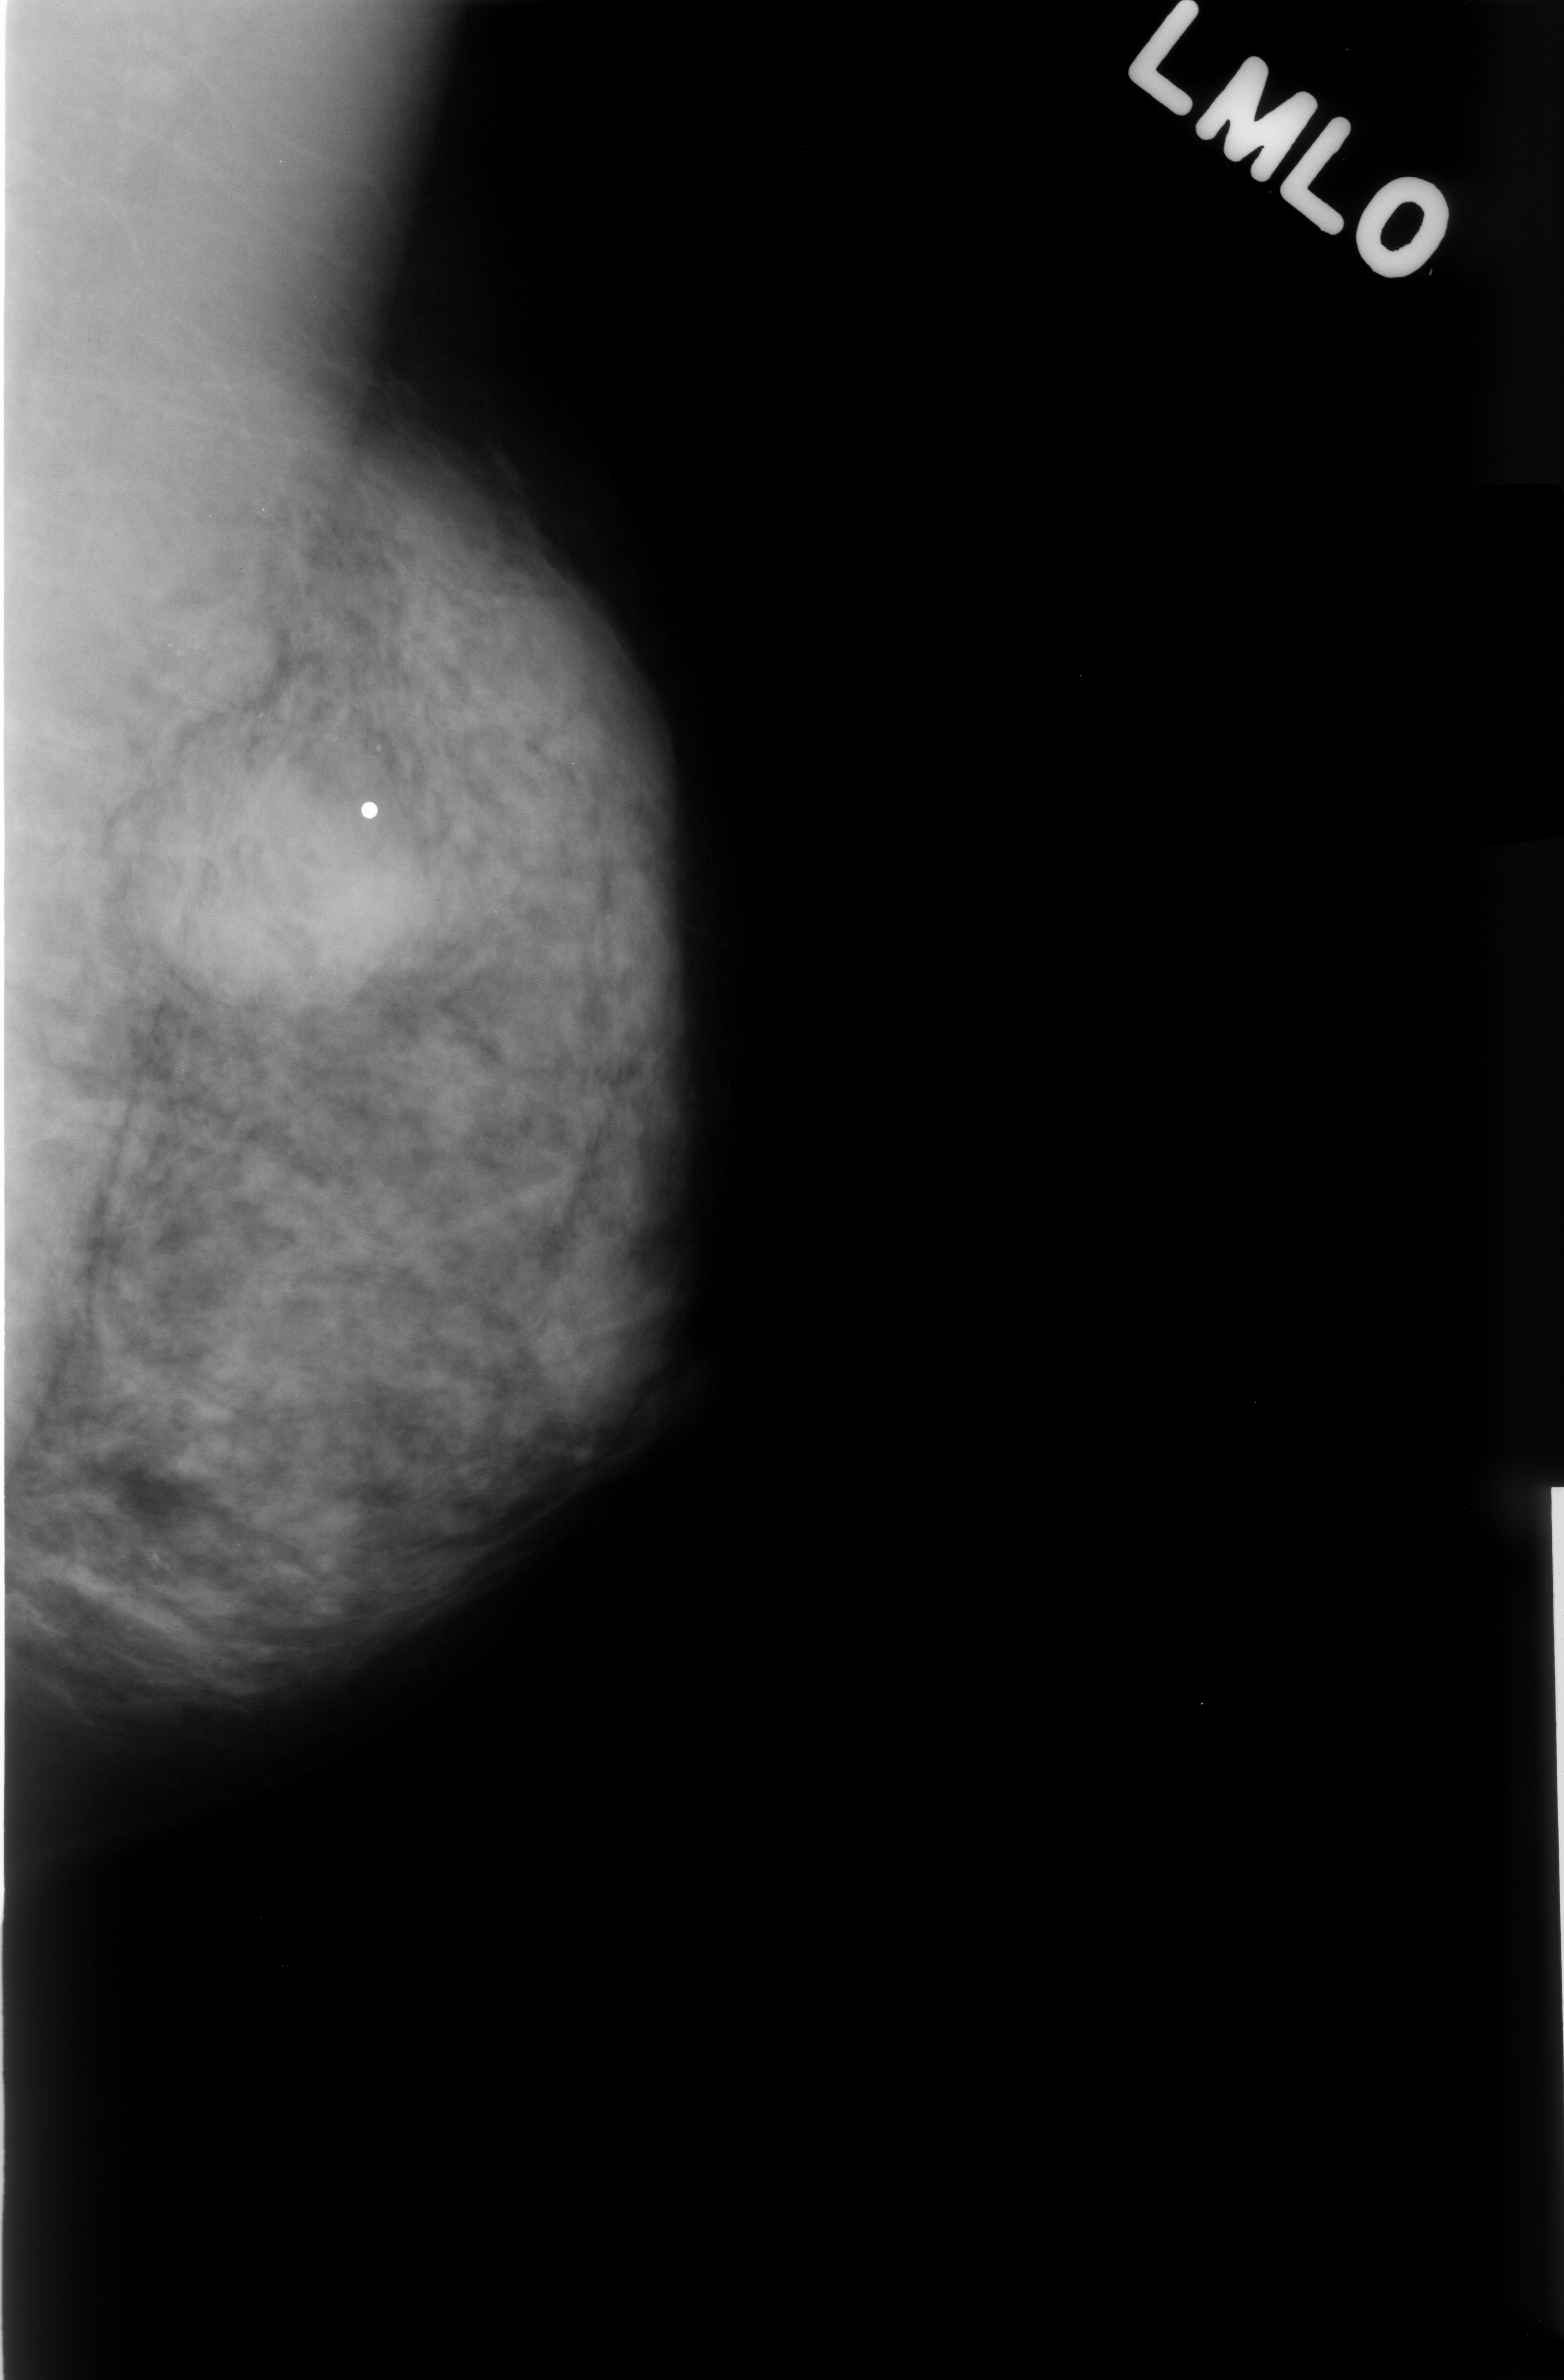
Scanned film-screen mammogram; left breast; mediolateral oblique (MLO) view.
- Finding: mass, shape round, margins microlobulated; BI-RADS assessment category 3; pathology (as recorded): benign.